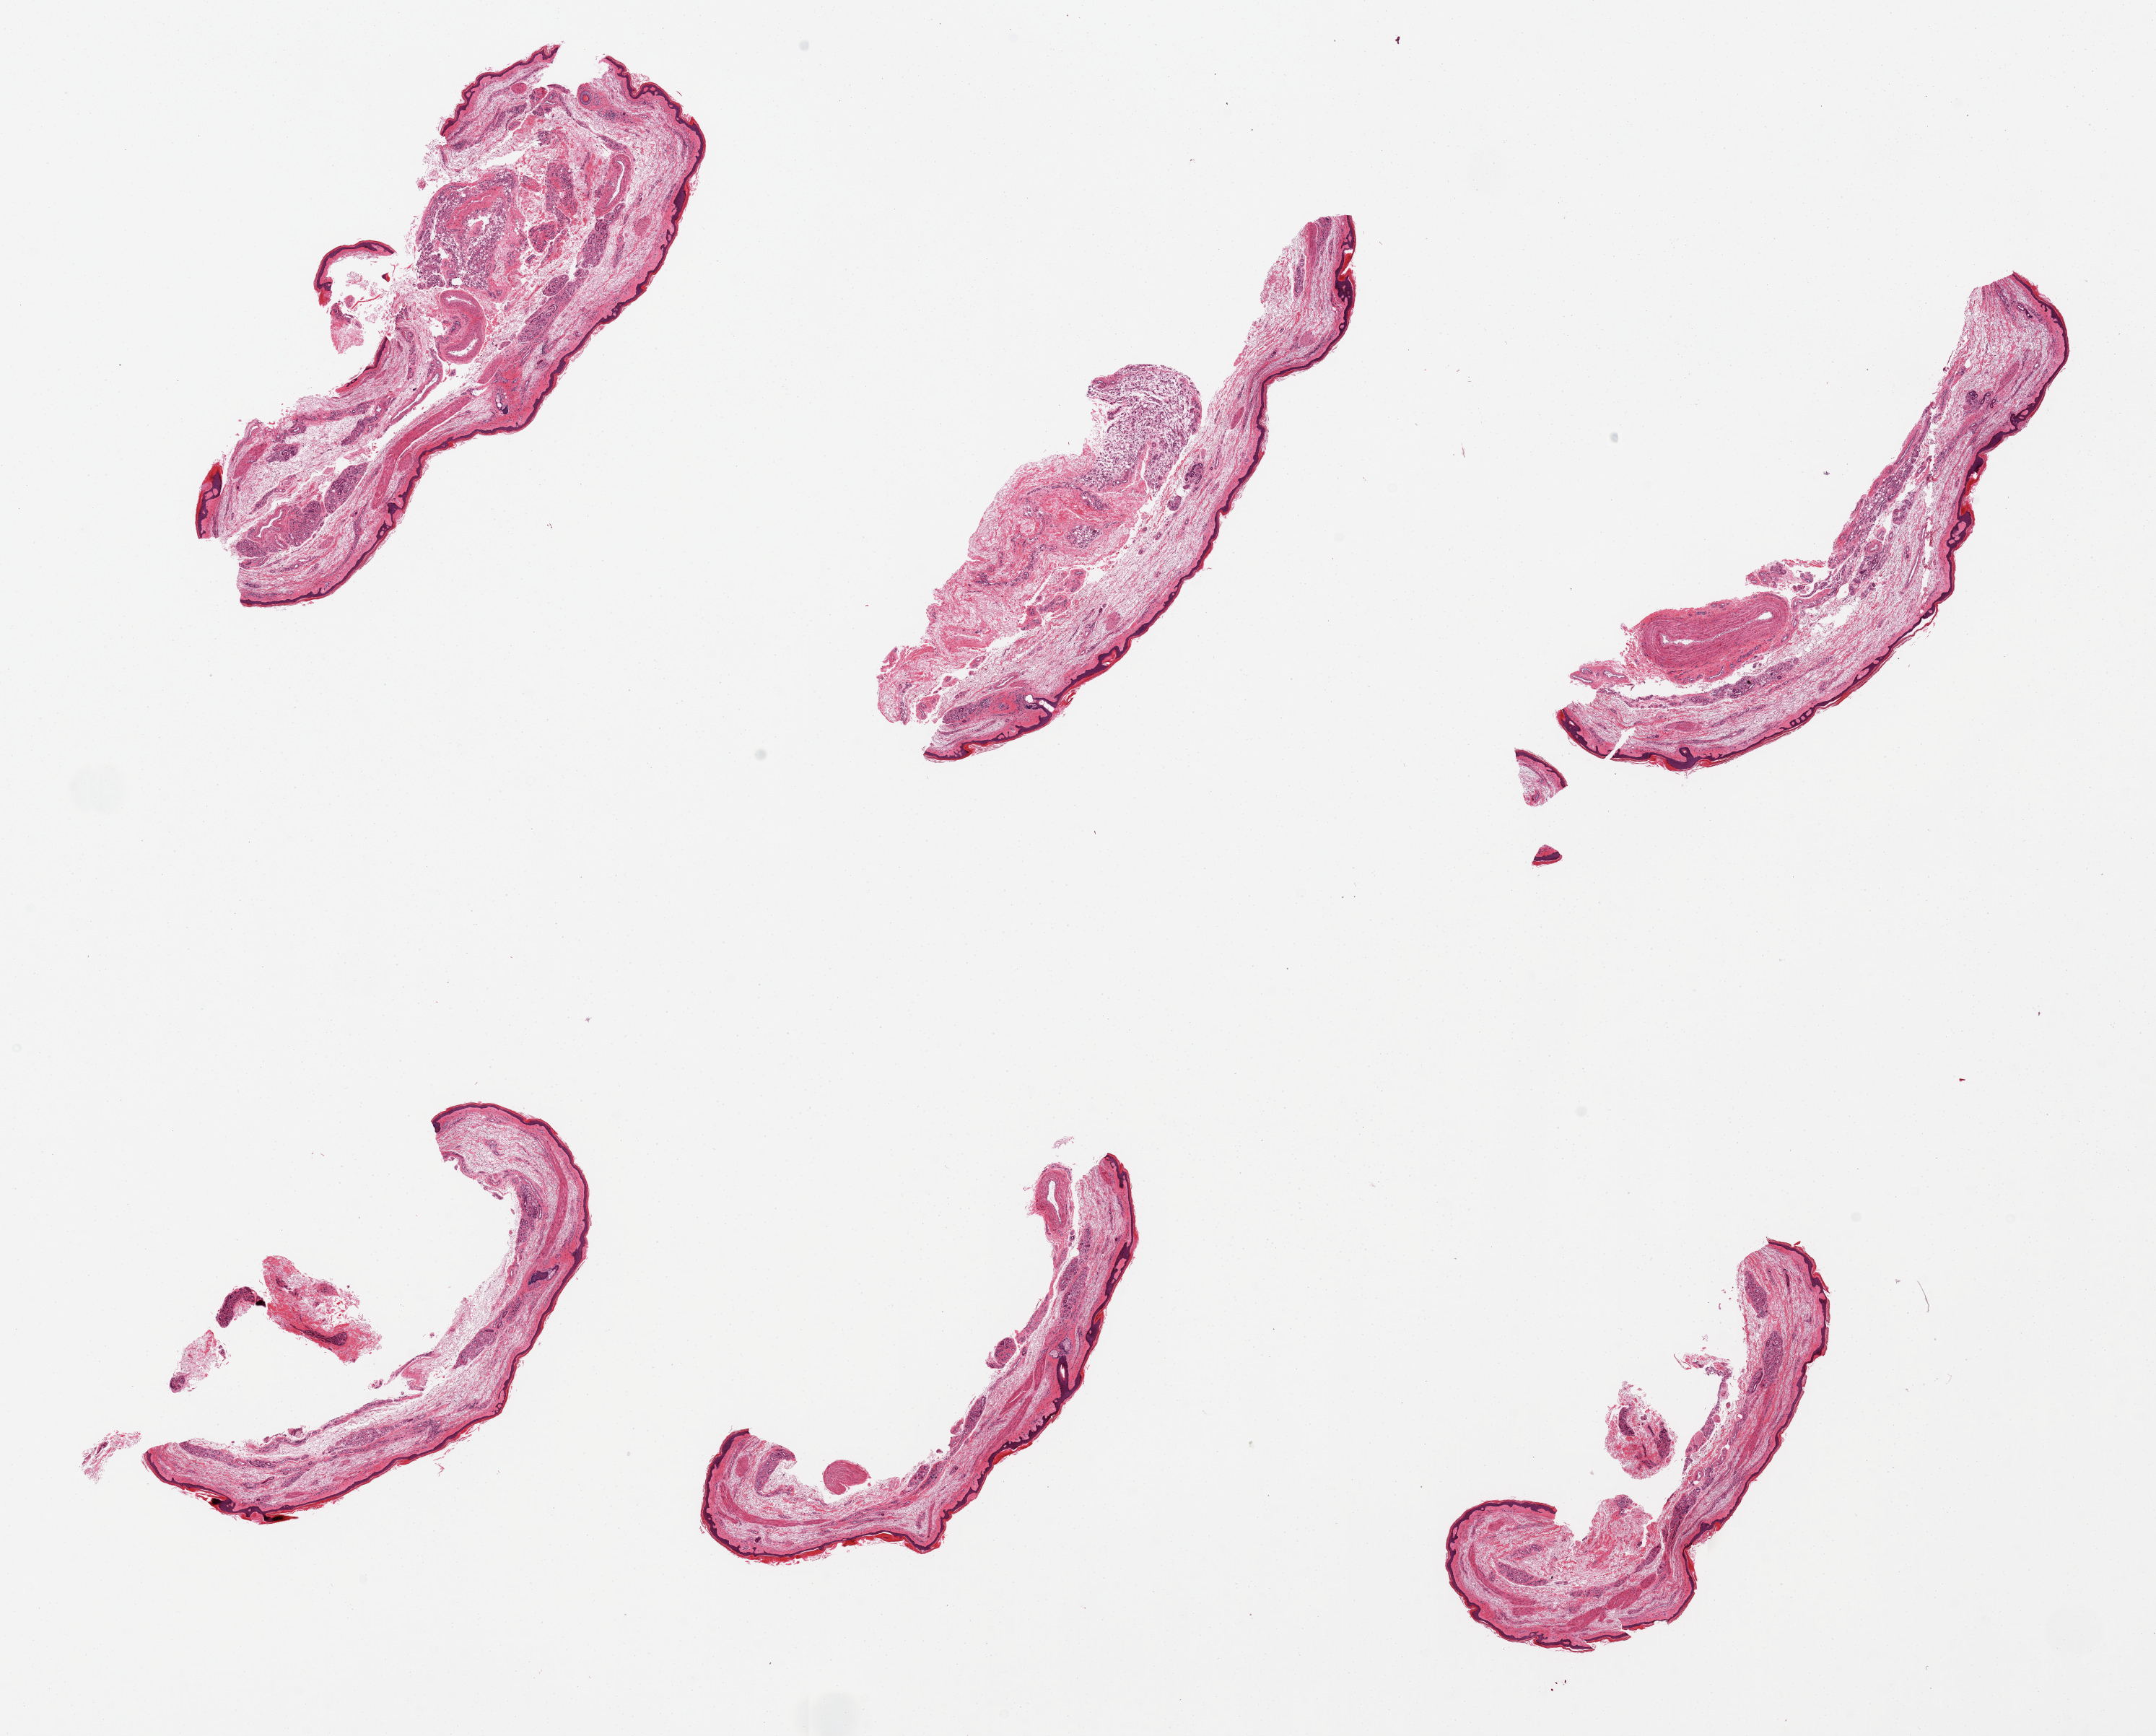
Digitized H&E-stained section, brightfield — shown as a low-resolution overview of the whole scanned area (about 23.6 x 19.0 mm), PAXgene-fixed paraffin-embedded (PFPE) section, sampled site (target tissue): skin of lower leg, donor tissue sample.
Reviewer comment on this tissue sample: 6 pieces; squamous epithelium is ~1.5-2% thickness, ~30-40 microns. Dermis appears edematous.